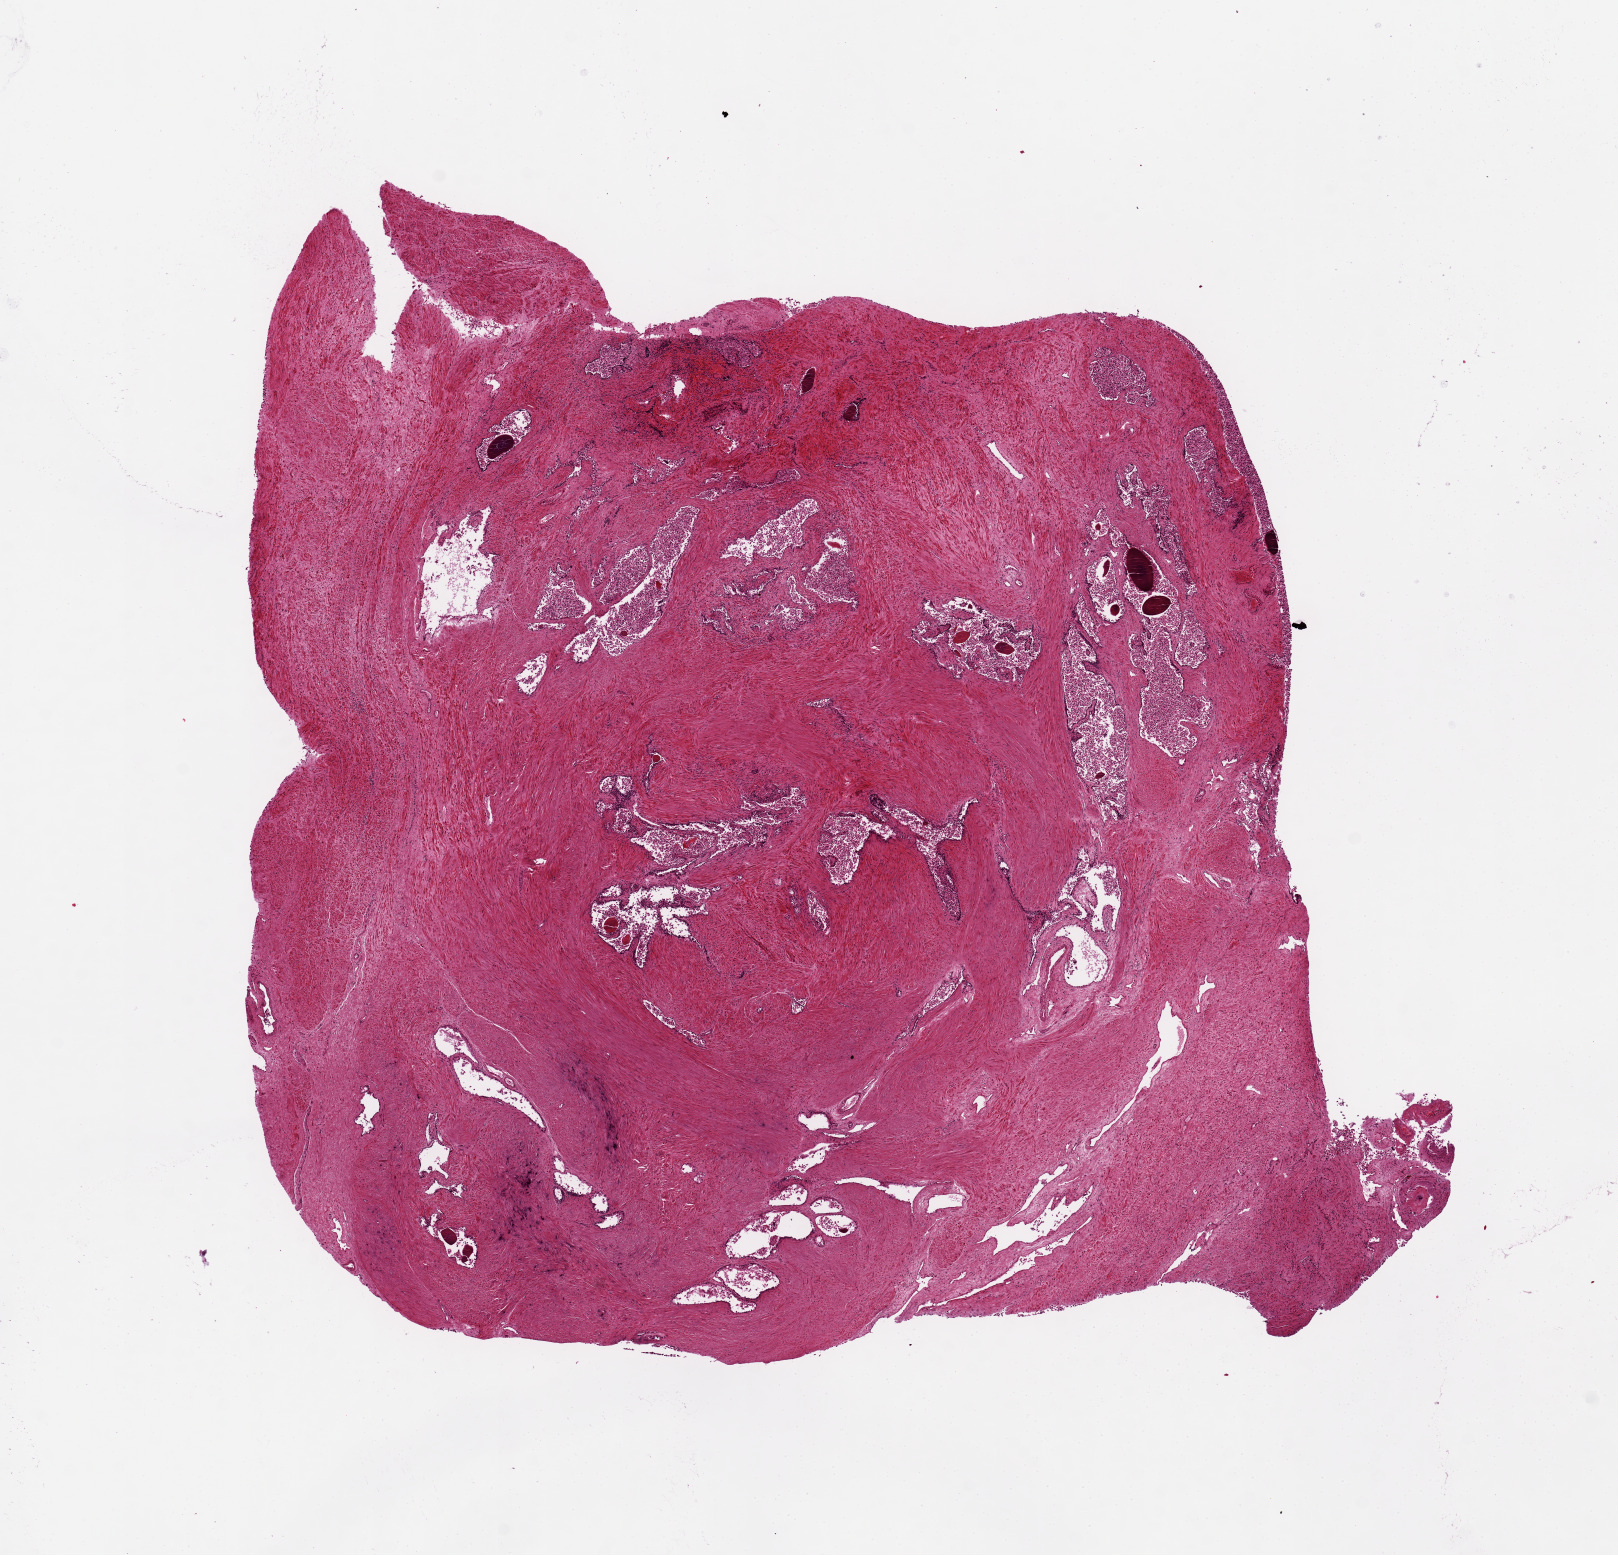
Hematoxylin and eosin (H&E) whole-slide image, shown as a low-resolution overview of the whole scanned area (about 12.8 x 12.3 mm). PAXgene-fixed, paraffin-embedded tissue. Sampled site (target tissue): prostate. Tissue donor sample. Male donor.
Review note (as recorded): Stromal hyperplasia and atrophy. 8x8mm.